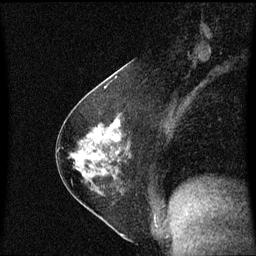
Breast MRI (dynamic contrast-enhanced), one sagittal slice. Slice 32 of 60 in the series (ordered by position). Dynamic contrast-enhanced series, image 2 of 3 at this slice position (ordered by acquisition). 1.5 T. TE 4.2 ms, TR 8.4 ms. 2 mm slice thickness. 256 × 256 image matrix, field of view 210 × 210 mm. Female patient, age 54 years. Case-level facts recorded for this patient, not image findings: setting: breast cancer imaged before/during neoadjuvant chemotherapy; receptor status: HER2-positive.
Annotated regions visible in this slice (semi-automatic segmentation, software-assisted and operator-edited):
- analysis volume of interest (the breast-tissue region the enhancement analysis was run in; not a lesion): bounding box [x1, y1, x2, y2] px = [59, 119, 133, 190]
- tumour enhancement mask (voxels above the 70 % enhancement threshold inside the analysis volume of interest): [115, 122, 120, 142]